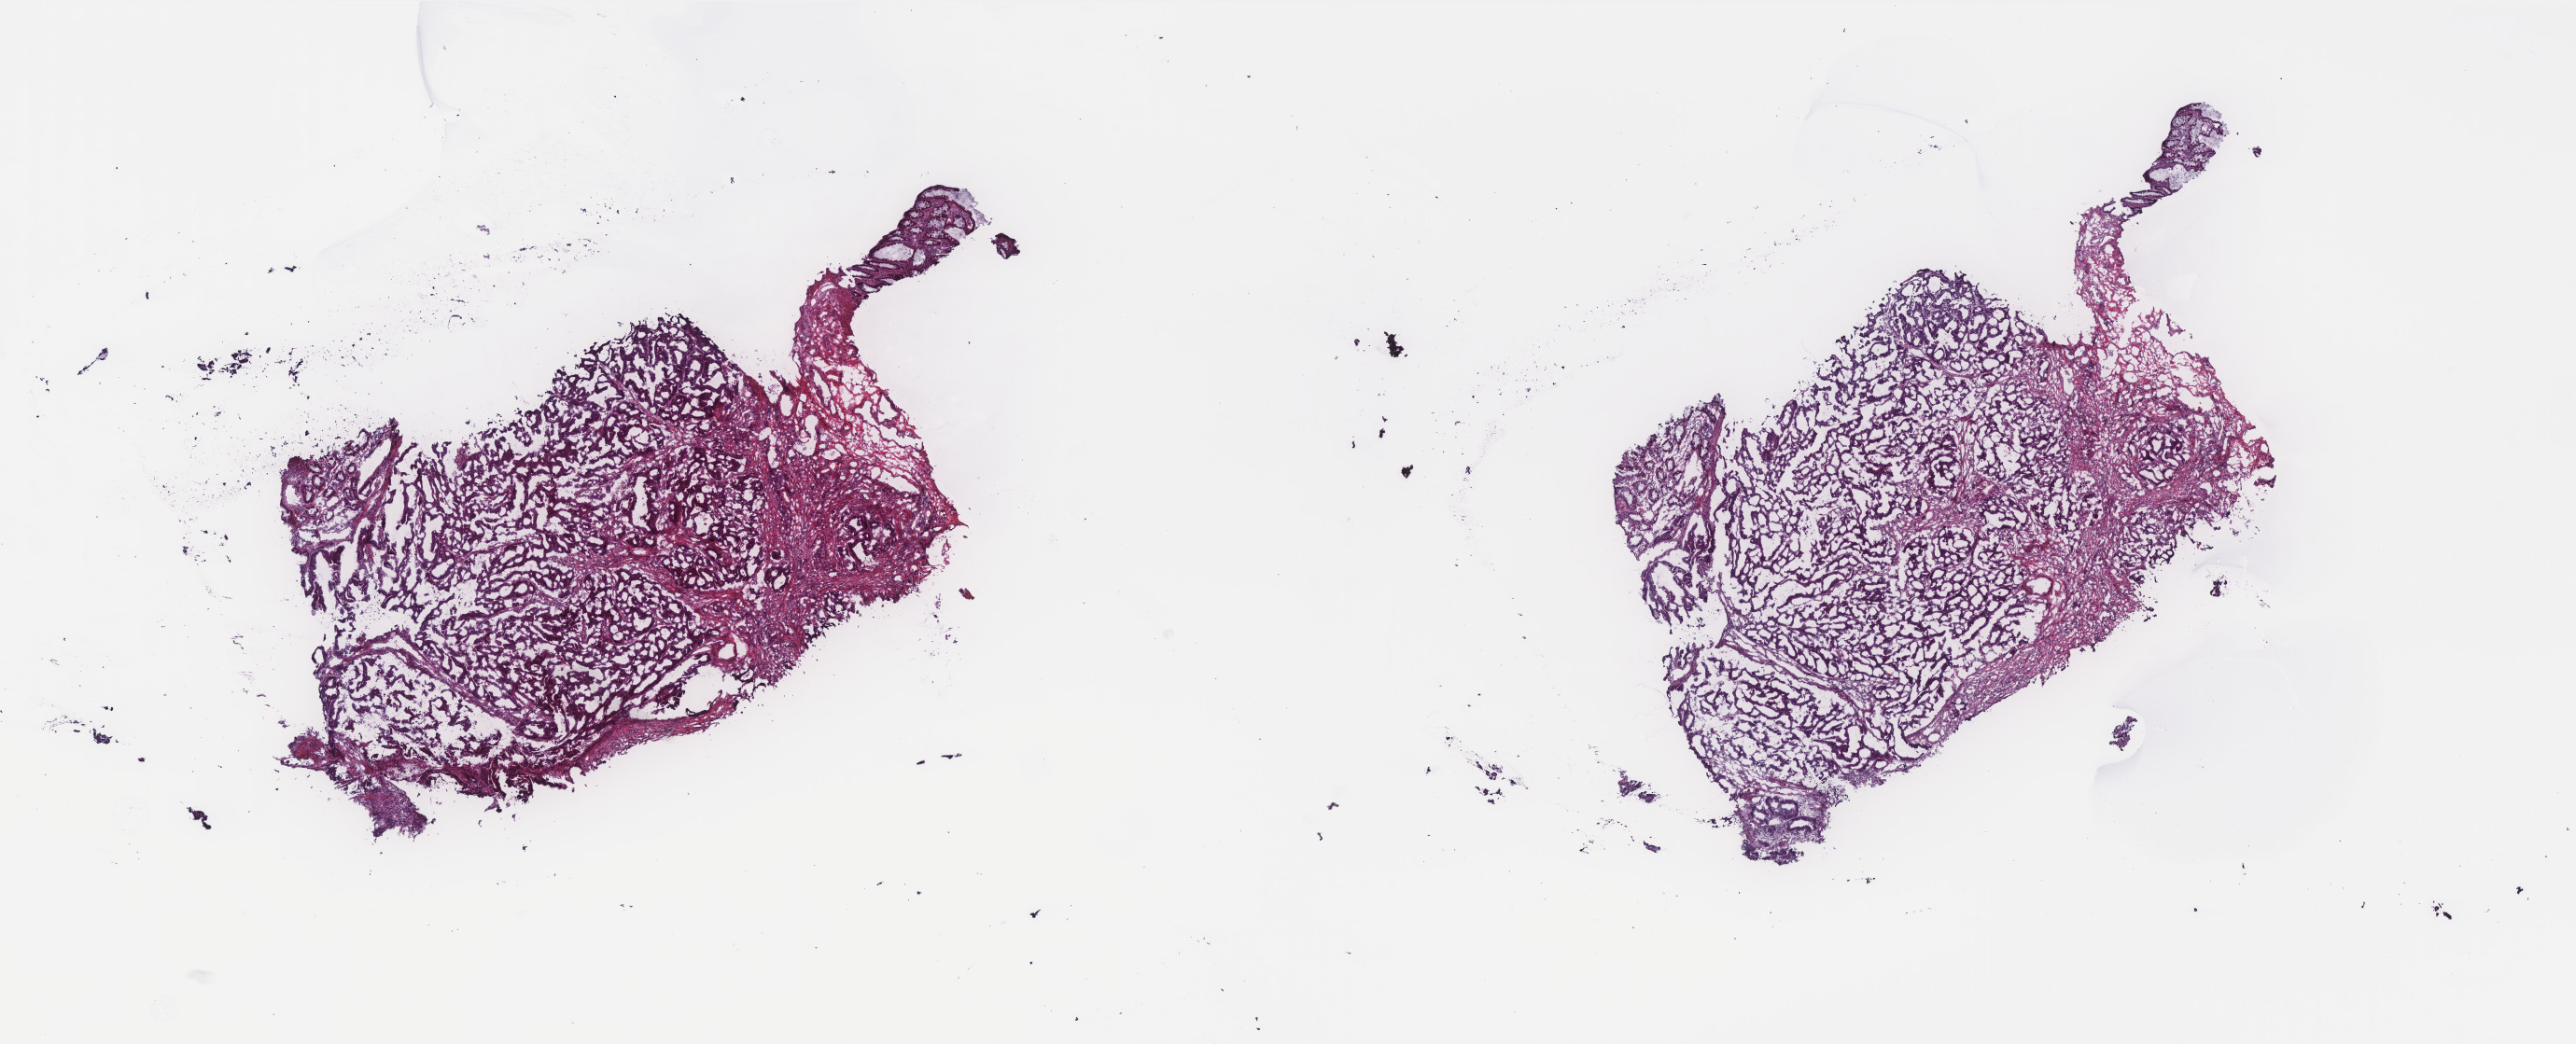
Whole-slide histology image, H&E-stained, shown as a low-resolution overview of the whole scanned area (about 22.1 x 9.0 mm, acquisition: 40x scan). Frozen section. Primary tumour sample from the rectum. Female, age 72 years at initial diagnosis. Pathologist review of this section (percent, as recorded): tumour cells 90%, tumour nuclei 75%.
Pathologic diagnosis: Adenocarcinoma, NOS (rectosigmoid junction).